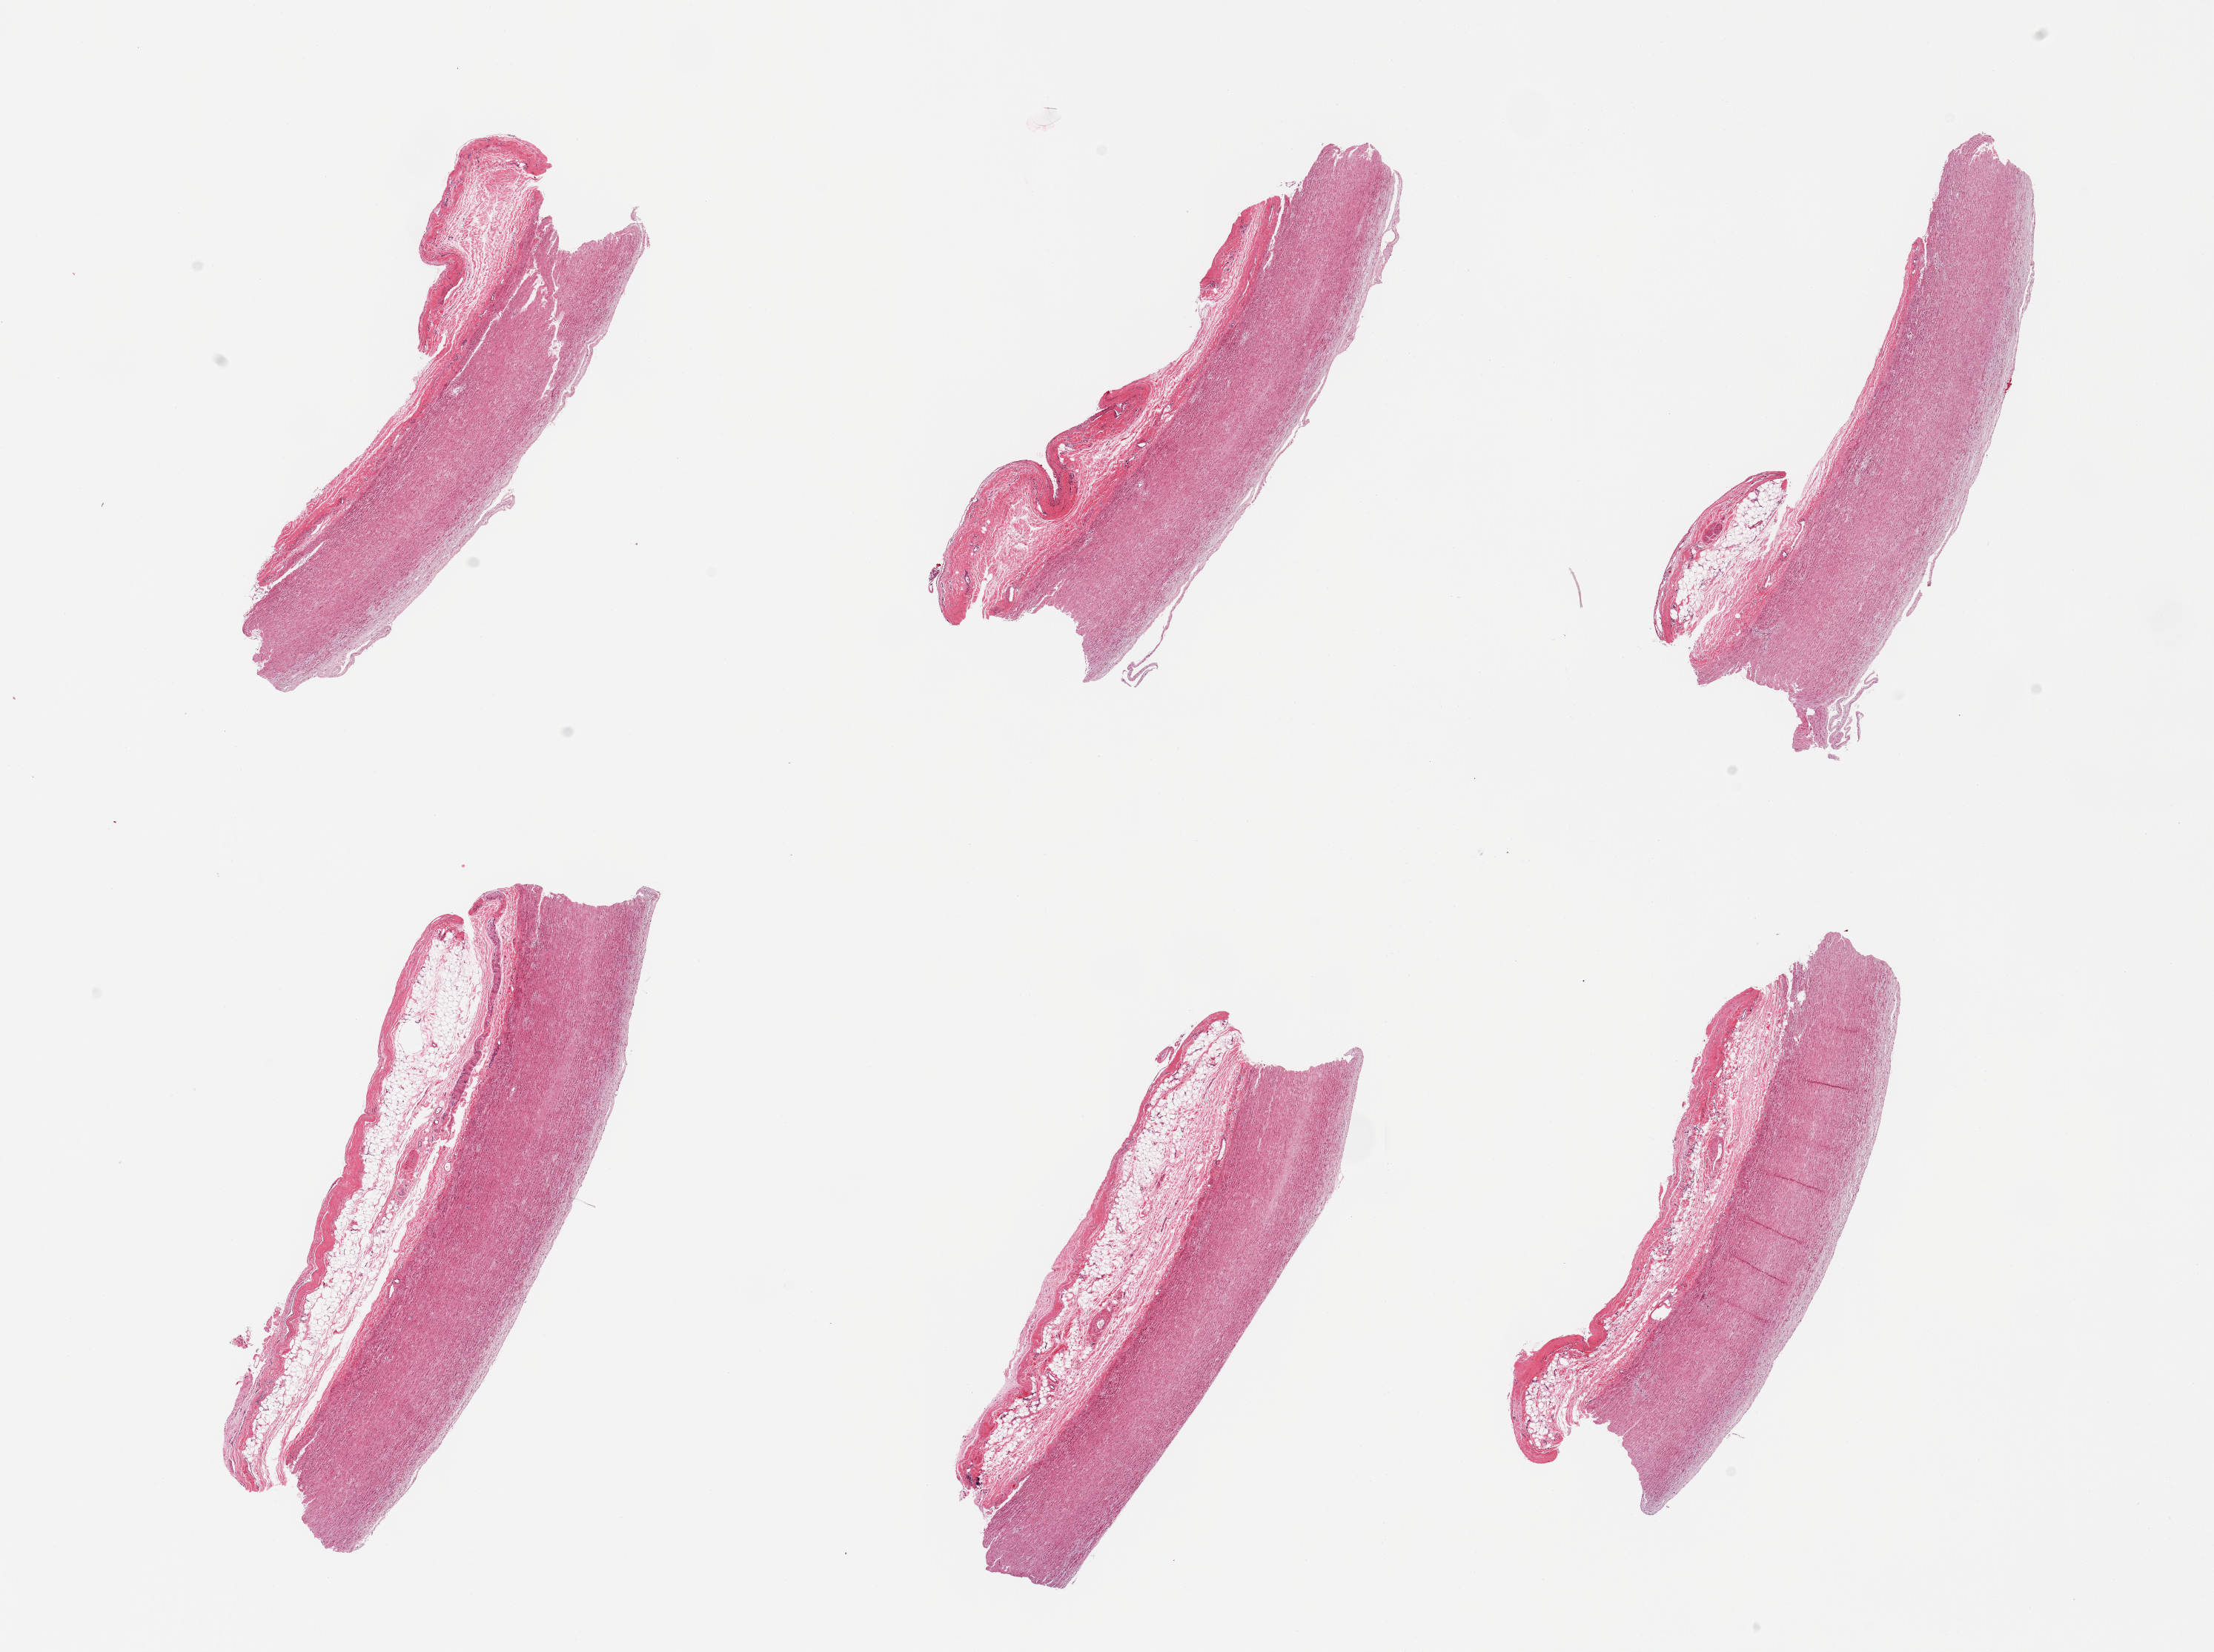
H&E whole-slide image — shown as a low-resolution overview of the whole scanned area (about 23.6 x 17.6 mm), PAXgene-fixed paraffin-embedded (PFPE) section, sampled site (target tissue): aorta, donor tissue sample.
Pathologist's review note for this sample: 6 pieces; thick fibroadipose adventitia (1 mm).